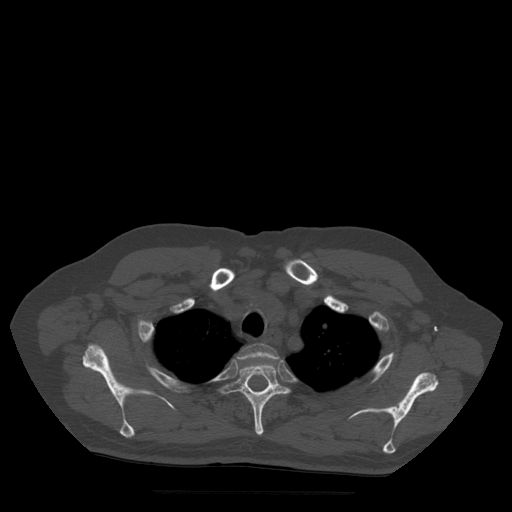
CT including the spine, one axial slice; position 411 of 522 along the scan axis; bone window (W 1800 / L 400 HU); 512 × 512 image matrix, field of view 420 × 420 mm. Patient age 72 years. From the clinical record (not read from this slice): primary cancer: prostate.
Annotated regions visible in this slice (semi-automatically segmented with operator editing):
- T2 vertebra: bounding box (x1, y1, x2, y2) in pixels: (237, 344, 280, 362)
- T3 vertebra: (219, 363, 290, 436)